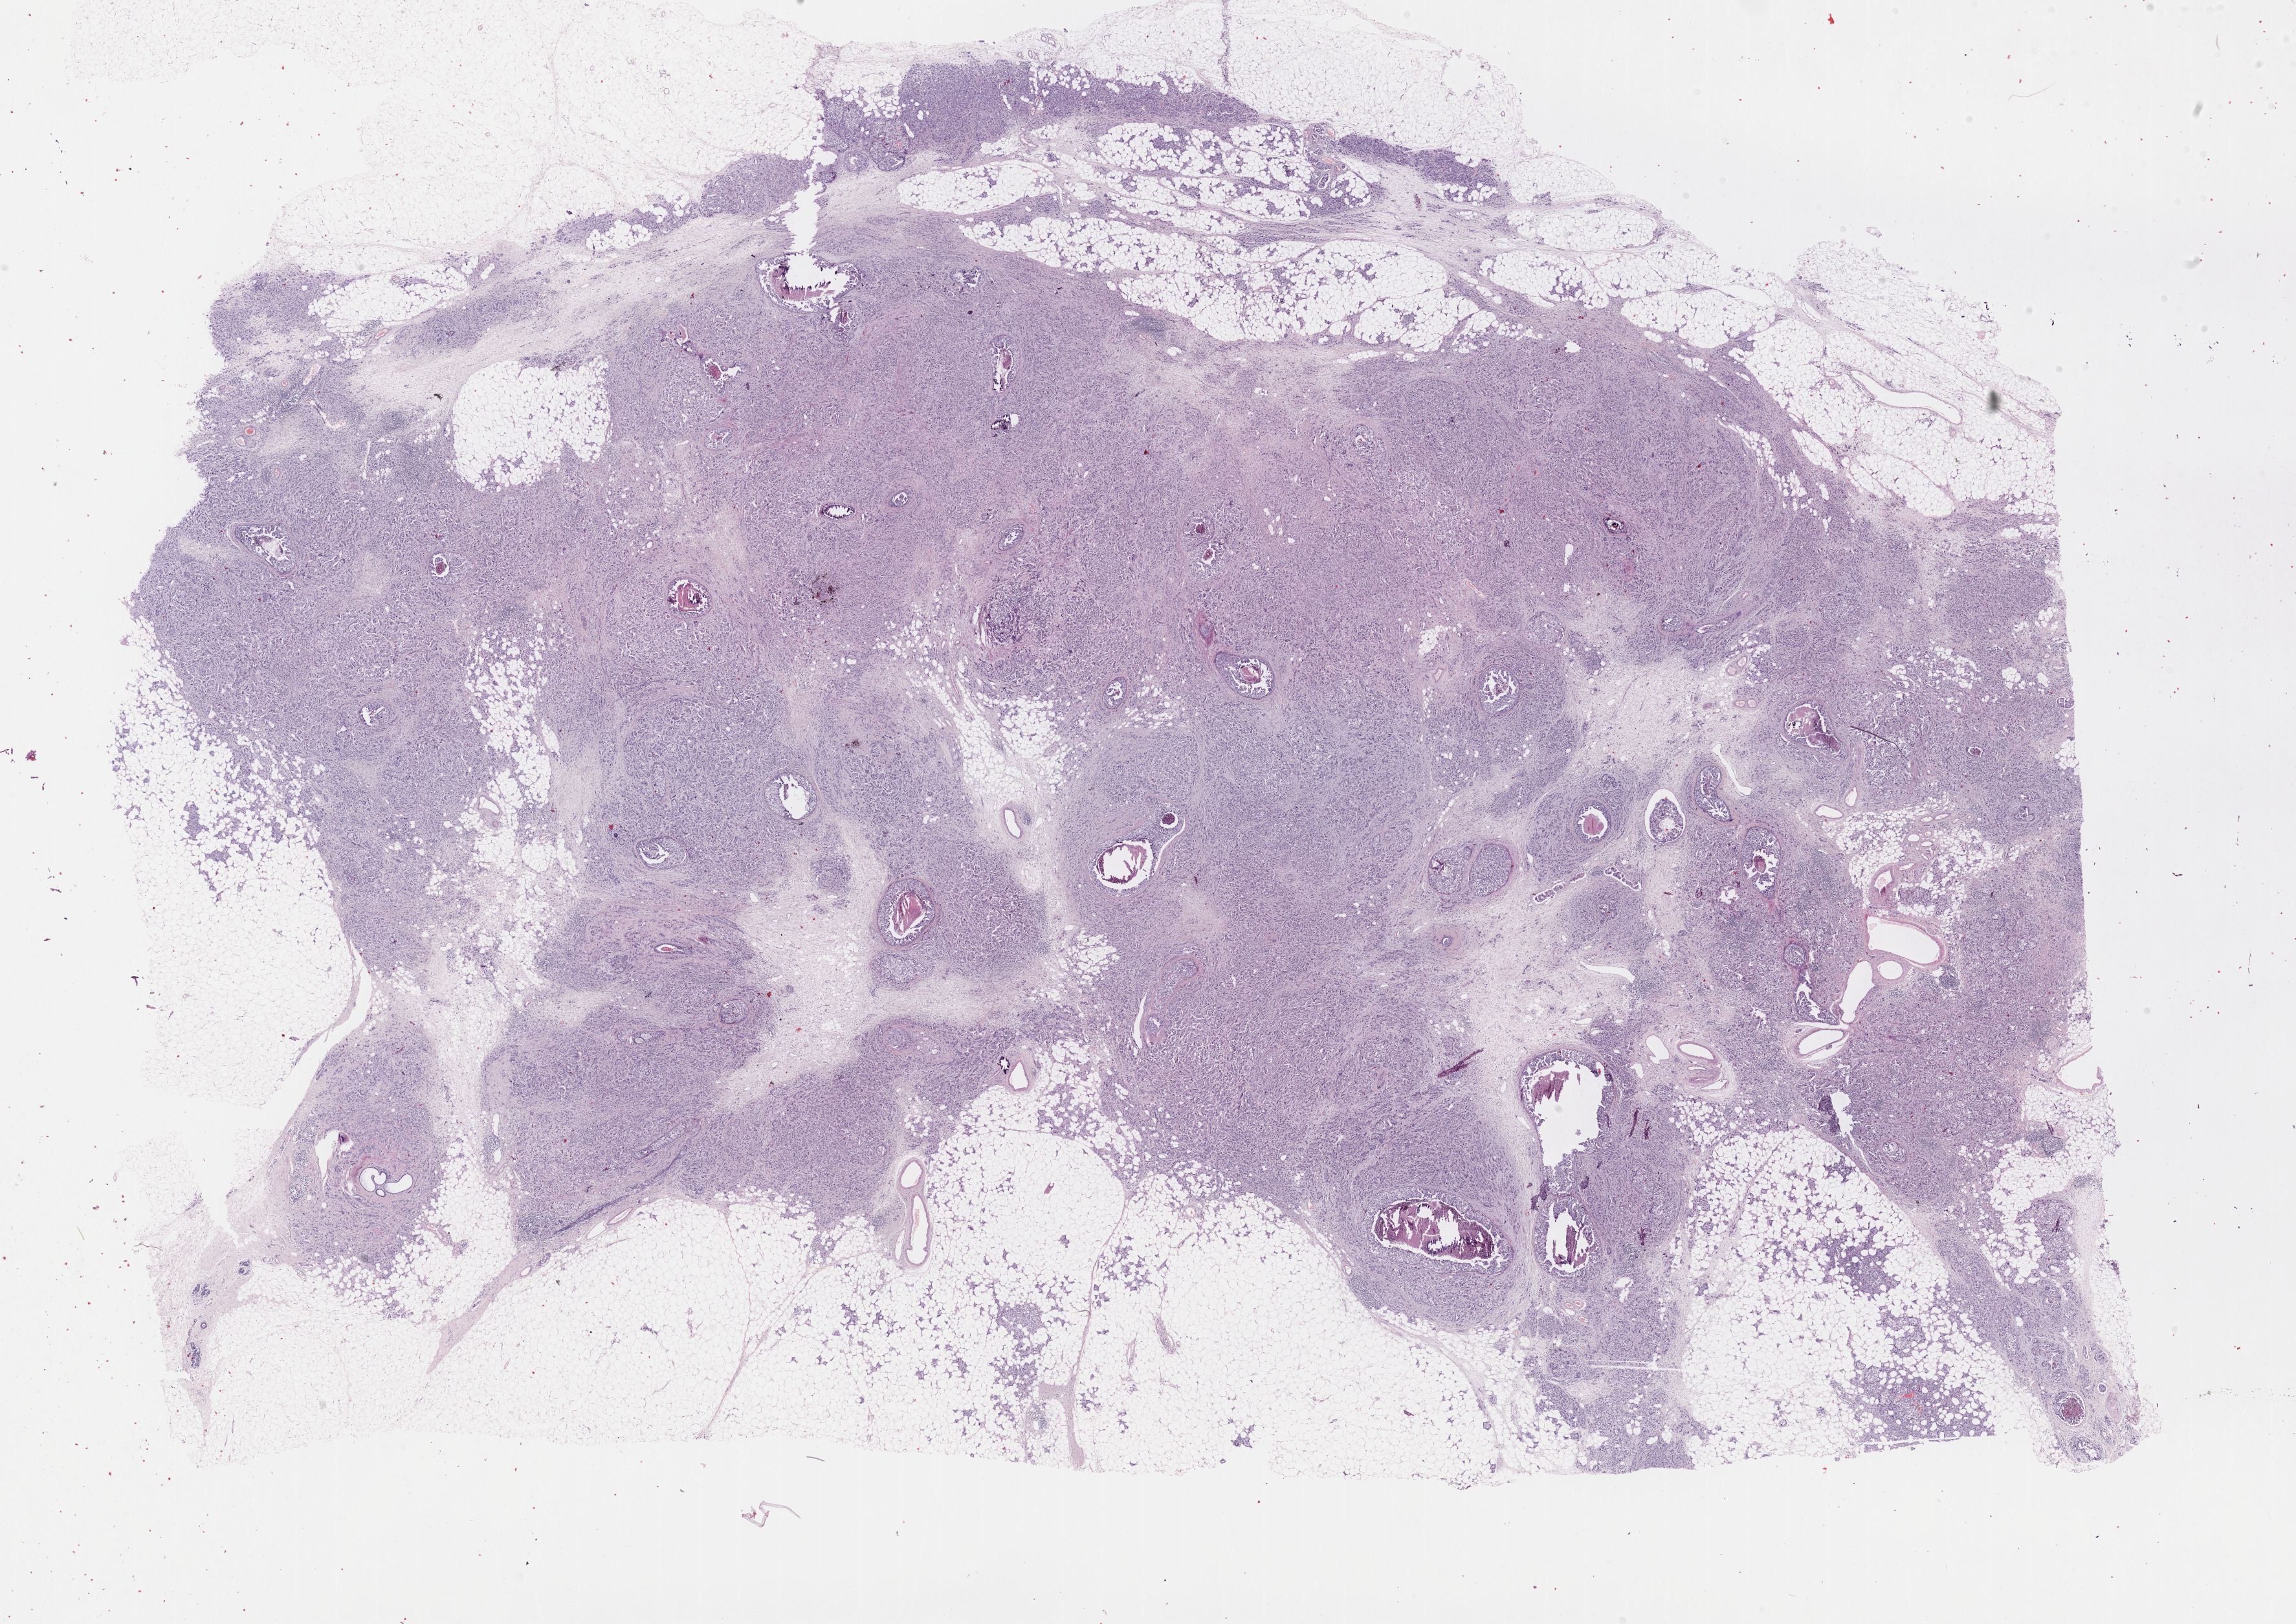
Digitized H&E tissue section (whole slide) — low-resolution overview of the scanned area, about 28.7 x 20.3 mm; formalin-fixed paraffin-embedded (FFPE) diagnostic section; primary tumour sample from the breast. Female patient; age at initial diagnosis 41 years.
* AJCC pathologic stage: IIIC (7th edition)
* pathologic diagnosis: Infiltrating duct carcinoma, NOS
* lymph nodes positive (case pathology): 11 of 11 examined
* TNM: T2 N3a M0